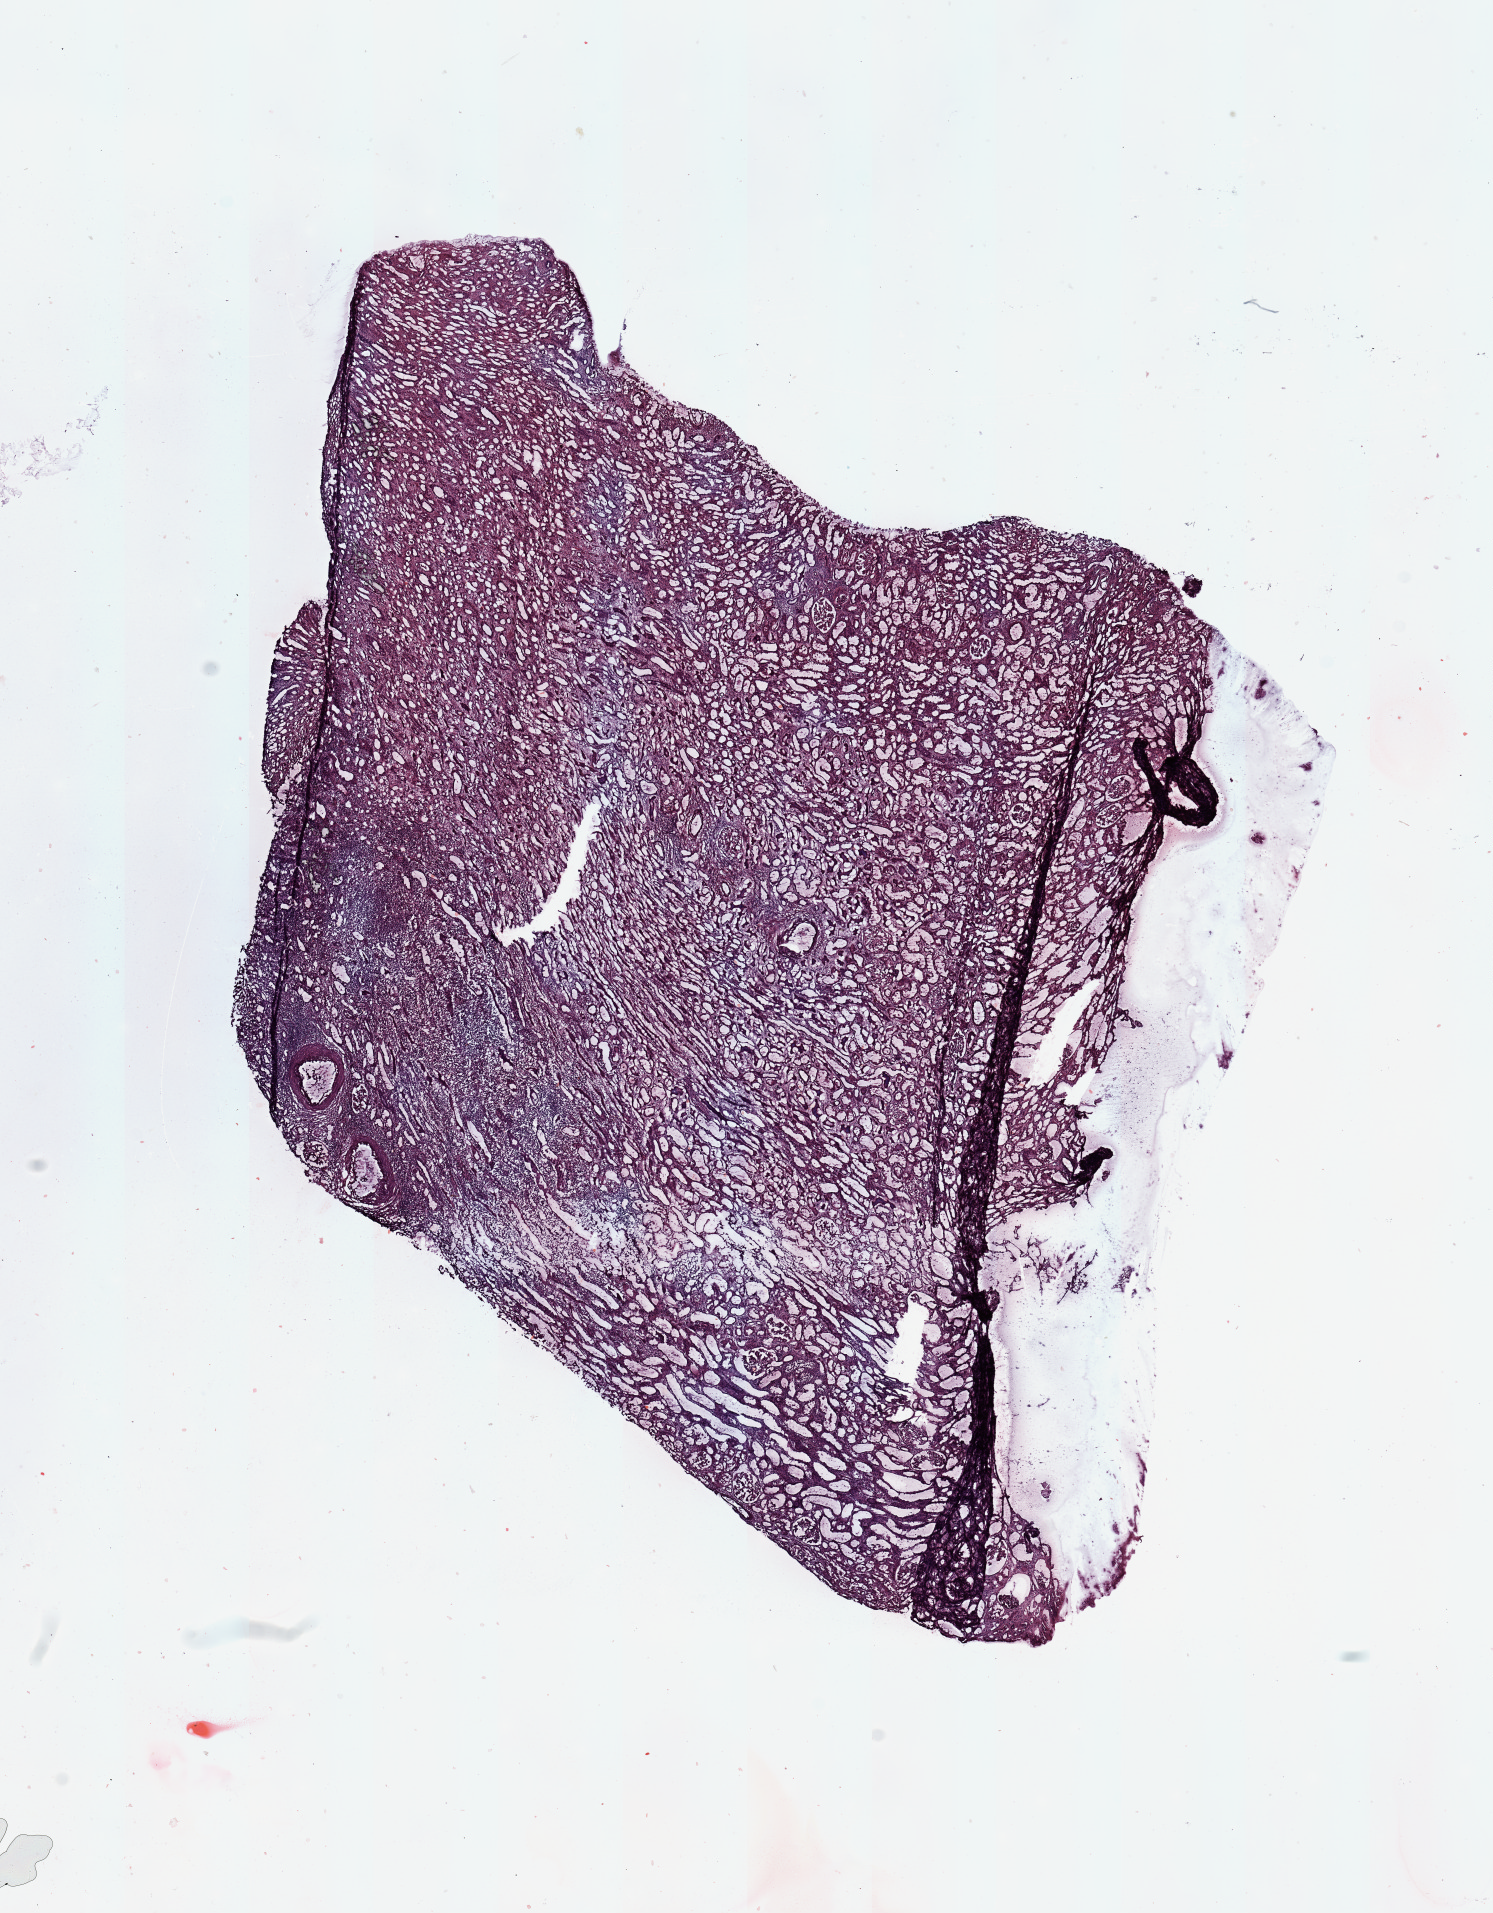
Whole-slide histology image, H&E, low-resolution overview of the scanned area, about 11.8 x 15.1 mm (from a 20x scan). Normal (non-tumour) tissue sample, sampled site: kidney. Patient: male, age 58 years.
- this section: normal (non-tumour) tissue from the same patient
- patient diagnosis: Renal cell carcinoma, NOS